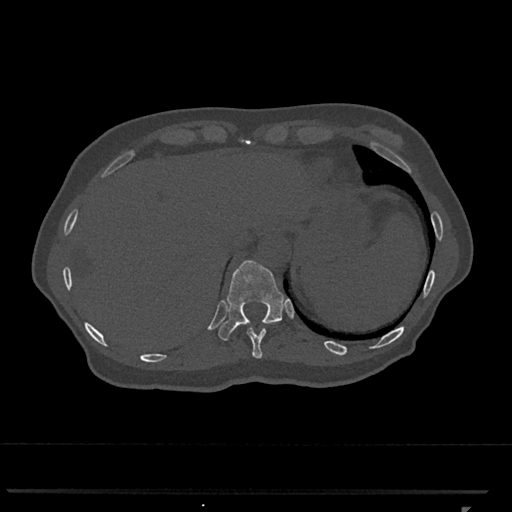
CT including the spine, one axial slice. Slice 537 of 793 in the series (ordered by position). Reconstruction kernel Br40s/3. Bone window (W 1800 / L 400 HU). 0.5 mm slice thickness. 512 × 512 image matrix, field of view 380 × 380 mm. Patient: female, 62 years. From the clinical record (not read from this slice): primary cancer: renal.
Outlined on this slice (semi-automatic segmentation, software-assisted and operator-edited):
- T10 vertebra: bounding box (x1, y1, x2, y2) in pixels: (247, 327, 267, 359)
- T11 vertebra: (218, 260, 284, 341)